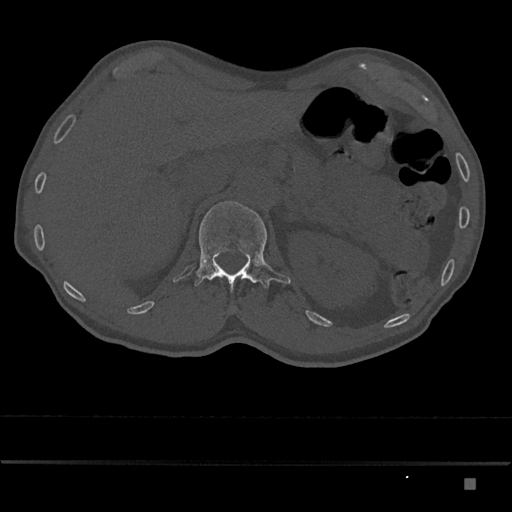
CT including the spine, one axial slice; reconstruction kernel Br40s/3; bone window (W 1800 / L 400 HU); 0.5 mm slice thickness; 512 × 512 image matrix, field of view 390 × 390 mm. Patient: male, 72 years. Case-level facts recorded for this patient, not image findings: primary cancer: prostate.
Structures marked on this image (semi-automatically segmented with operator editing):
- L1 vertebra: box from (x=194, y=201) to (x=291, y=292) px